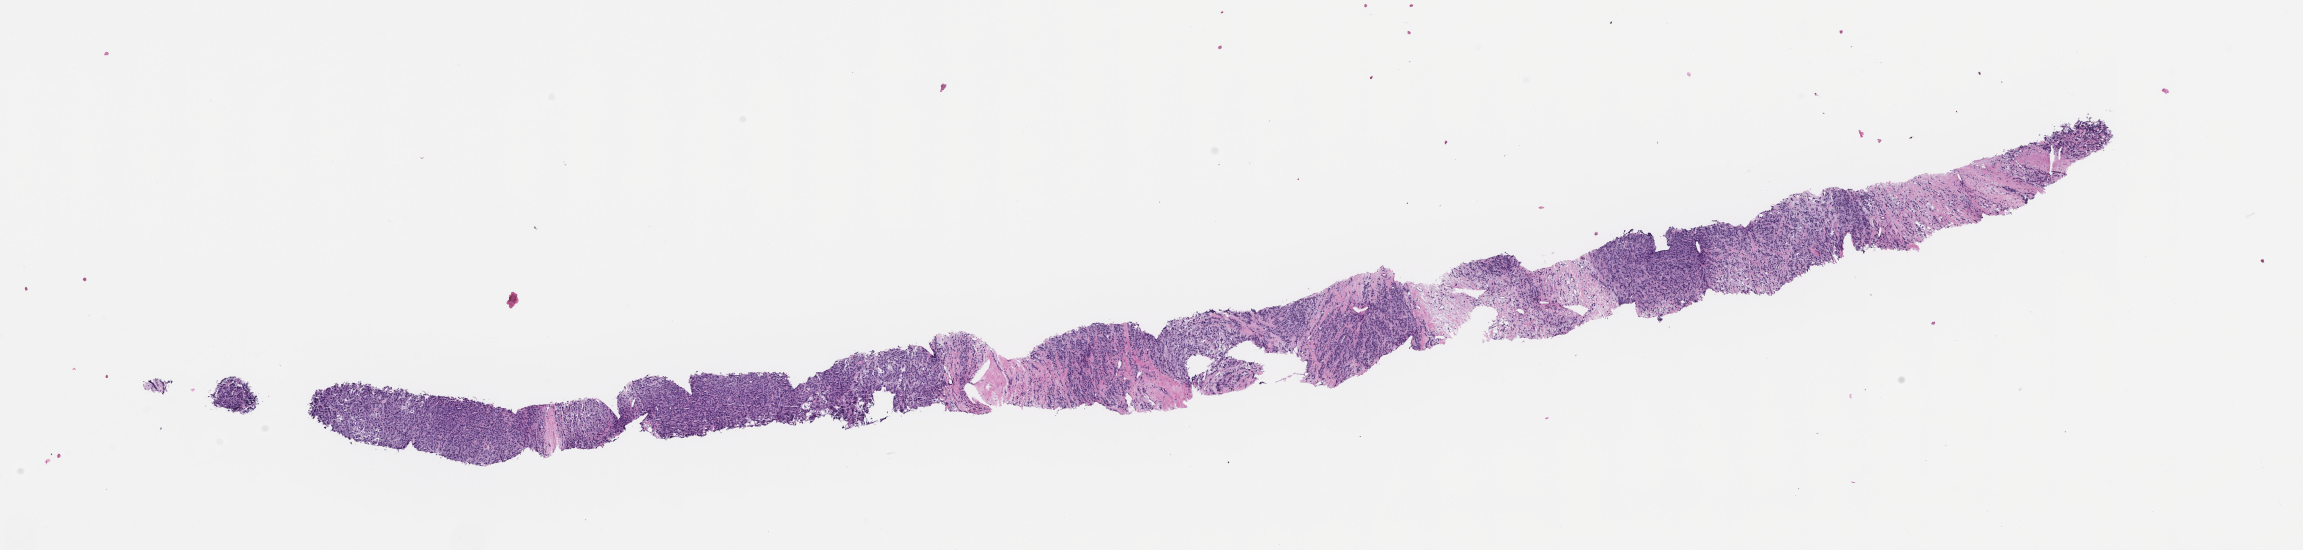
Whole-slide image, H&E stain, whole scanned area (about 18.6 x 4.4 mm) shown as a low-resolution overview; formalin-fixed paraffin-embedded section; tissue site: prostate. Male patient.
This section: primary tumor. Diagnosis: Prostate Carcinoma.